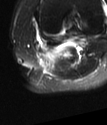
MRI of an extremity soft-tissue mass, one axial slice; slice 54 of 78 in the series (ordered by position); T2-weighted fat-saturated; MR volume resampled by the dataset authors to the PET/CT grid (not the native acquisition matrix); 107 × 125 image matrix, field of view 104 × 122 mm. Female patient. Case-level facts recorded for this patient, not image findings: histological type: extraskeletal high grade osteogenic sarcoma; grade: high; site of the primary tumour: left calf.
Structures marked on this image (expert contour drawn on MRI and transferred to this co-registered scan by the dataset authors):
- gross tumour volume (mass): bounding box (x1, y1, x2, y2) in pixels: (48, 50, 59, 62)